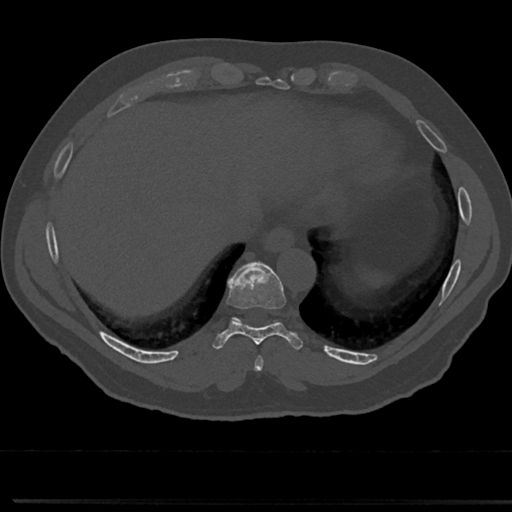
CT including the spine, one axial slice. Position 299 of 817 along the scan axis. Bone window (W 1800 / L 400 HU). 0.5 mm slice thickness. 512 × 512 image matrix. Patient: male, 61 years. Case-level facts recorded for this patient, not image findings: primary cancer: prostate.
Outlined on this slice (semi-automatically segmented with operator editing):
- T8 vertebra: bounding box <236,326,283,357> (left, top, right, bottom; pixels)
- T9 vertebra: <232,266,283,330>